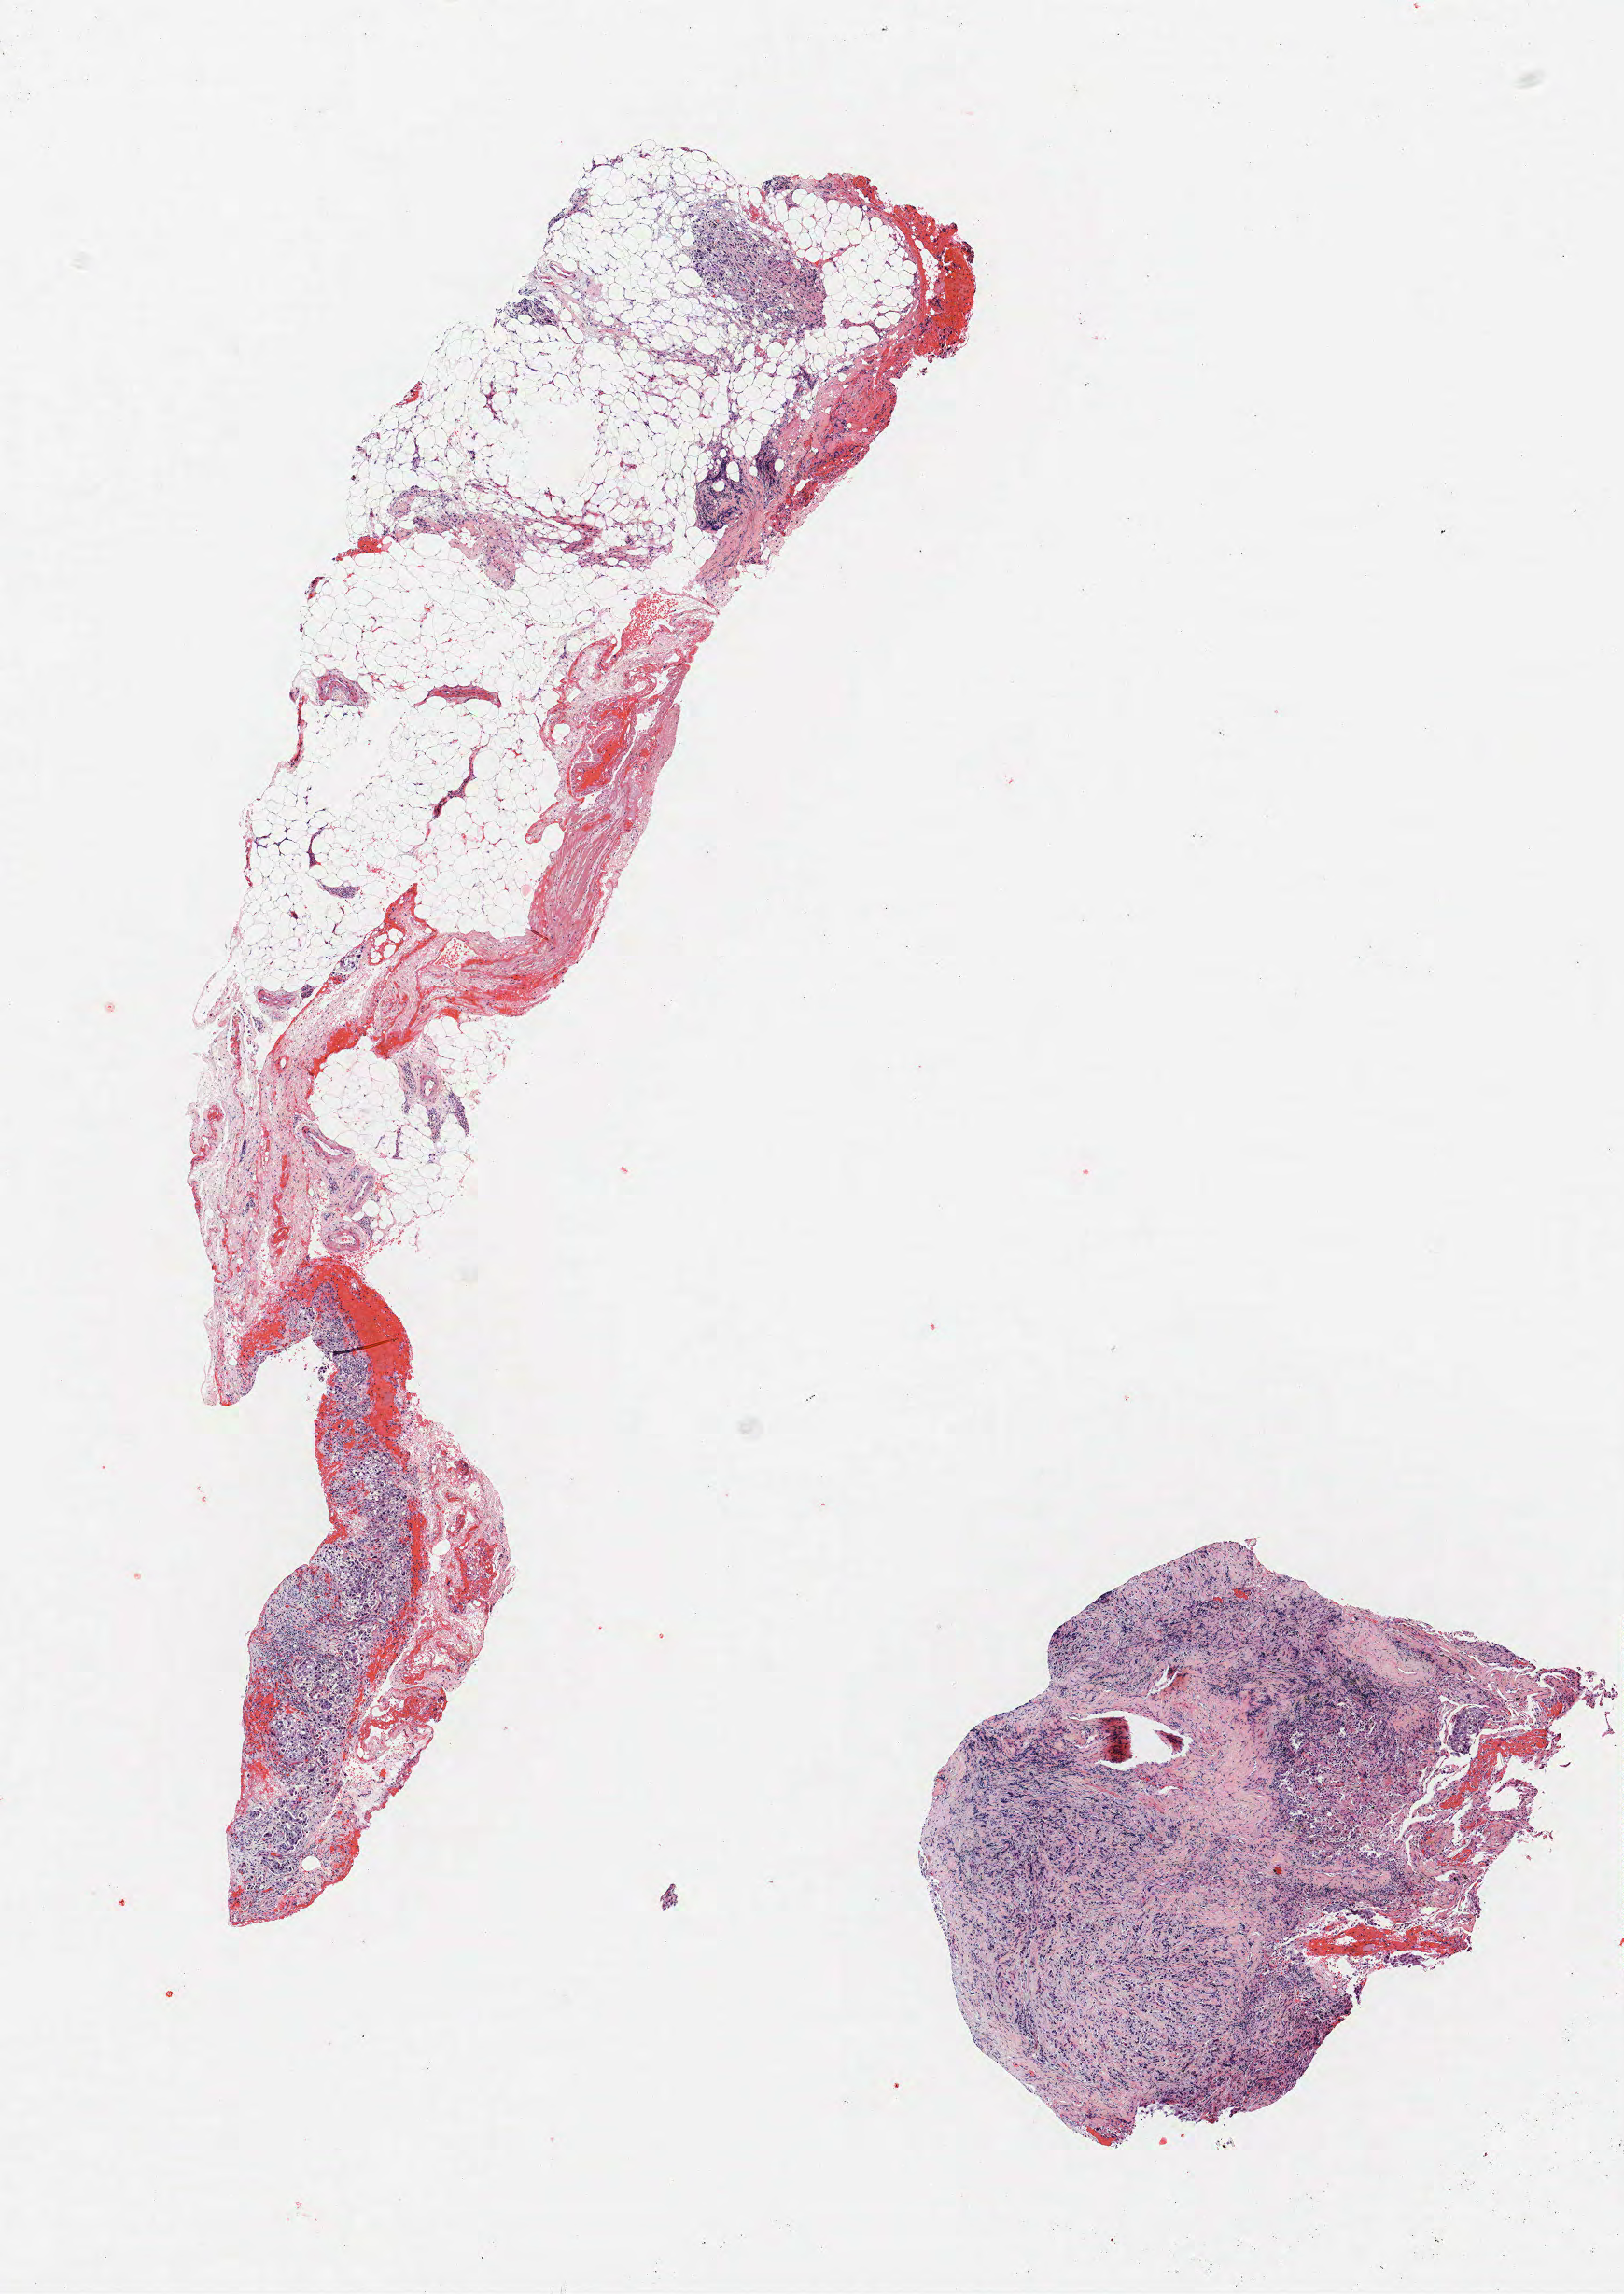
Hematoxylin and eosin (H&E) stained whole-slide image — whole scanned area (about 7.0 x 9.8 mm, from a 40x scan) shown as a low-resolution overview, FFPE section, lung. Male patient, aged 73 at enrolment. Former smoker at enrolment. Grade: cannot be assessed (GX).
Primary tumour location (clinical record): left hilum. Participant's lung-cancer diagnosis: Adenocarcinoma, NOS. Stage (AJCC 6th edition): IV. ICD-O-3 topography: main bronchus (C34.0).